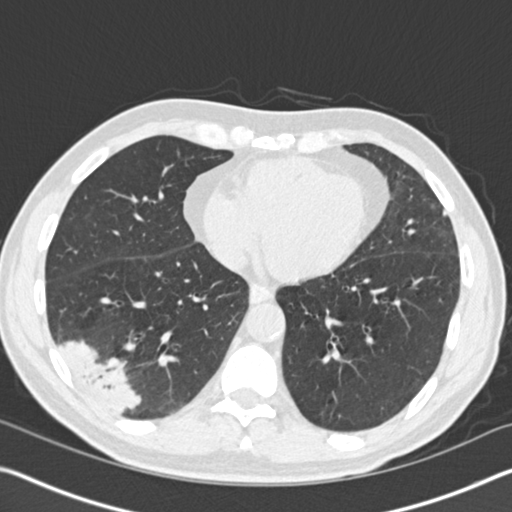
Axial slice from a low-dose chest CT screening exam. First (baseline) screen. Lung window (W 1500 / L -600 HU). Slice 104 of 161 in the series. 512 × 512 image matrix, field of view 340 × 340 mm. Male, age 61 years at enrolment. Current smoker at enrolment.
- Expert-annotated lung lesion, bounding box [x1, y1, x2, y2] px = [36, 310, 151, 421].
- Reader record for this screening exam (exam-level; its link to the box is not recorded): non-calcified nodule or mass ≥4 mm, right lower lobe, 52 × 36 mm, spiculated (stellate) margins, soft tissue attenuation.
- Lung cancer was diagnosed 392 days after this screen (after the second annual screen): bronchiolo-alveolar adenocarcinoma, NOS, right lower lobe, moderately differentiated (G2), stage IIIB (AJCC 6th edition), 90 mm at pathology.